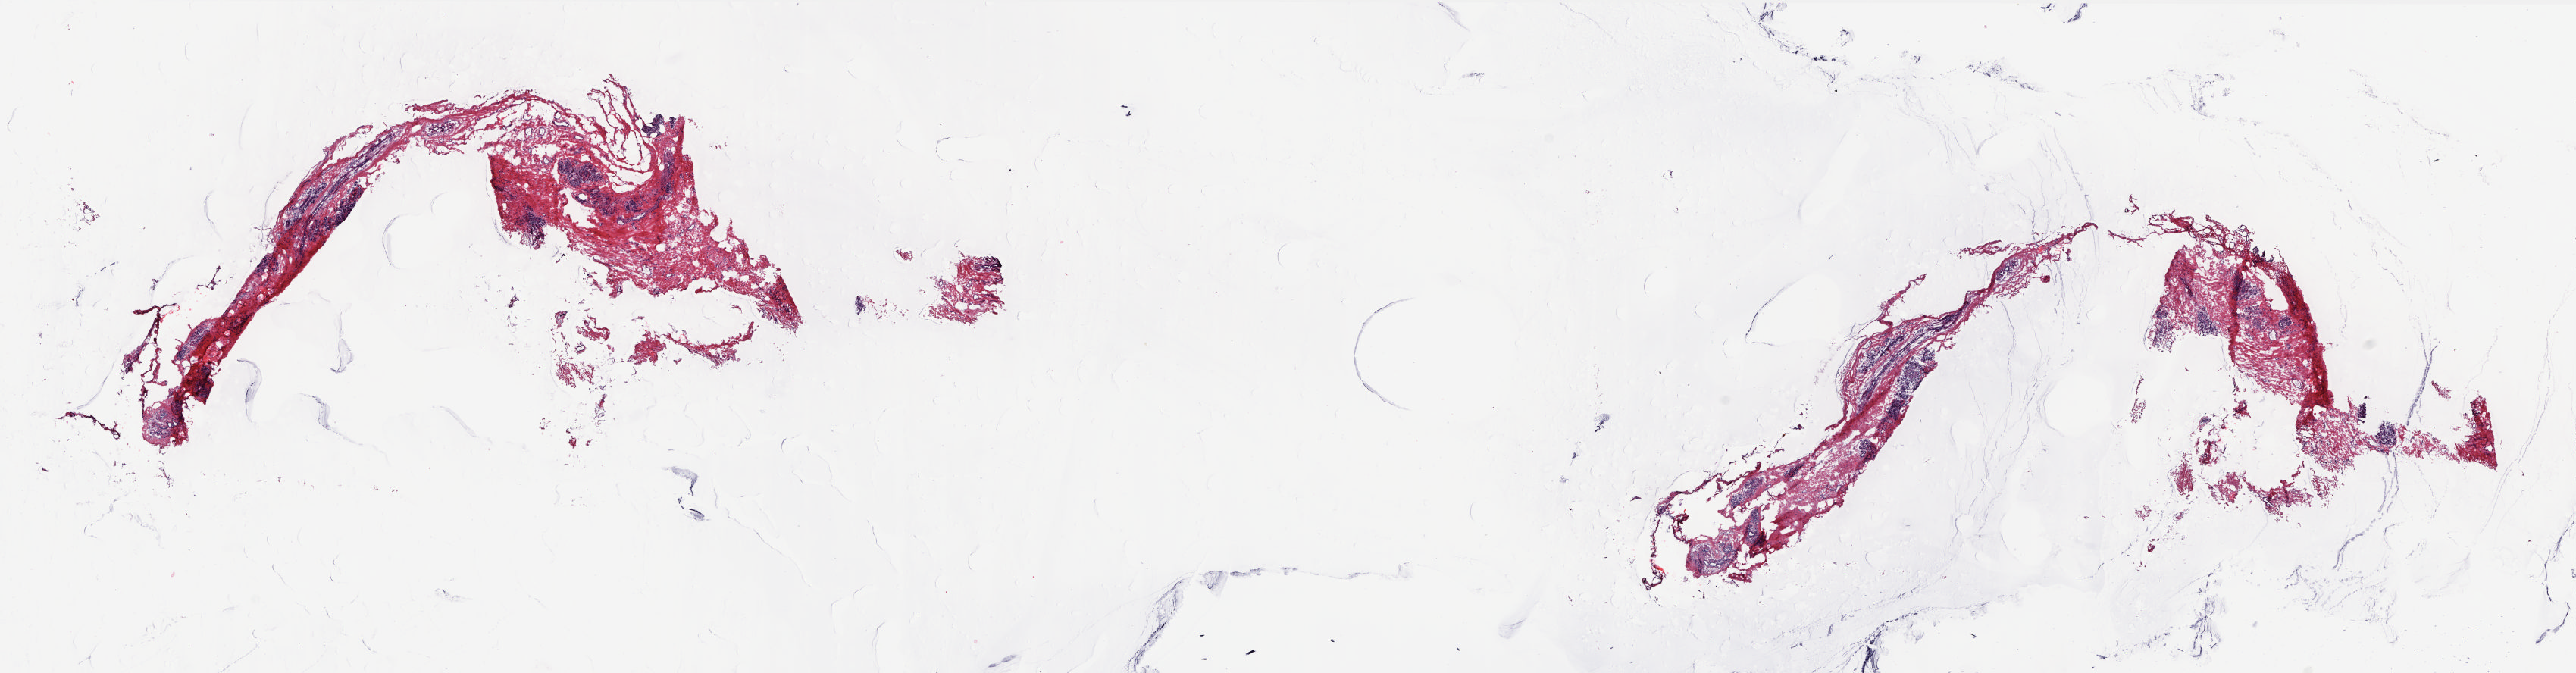
Whole-slide histology image, Hematoxylin and eosin (H&E) stained — shown as a low-resolution overview of the whole scanned area (about 27.4 x 7.2 mm). Frozen section from the top of the tissue portion. Sample: solid tissue normal (non-tumour tissue), breast. Patient: female, age at initial diagnosis 52 years. Pathologist review of this section (percent, as recorded): tumour cells 0%, tumour nuclei 0%, normal cells 25%, stromal cells 75%, necrosis 0%. Infiltration values recorded for this section: lymphocyte infiltration 2%, monocyte infiltration 0%, neutrophil infiltration 0%.
This section: solid tissue normal sample (biorepository sample class). Patient diagnosis: Infiltrating duct carcinoma, NOS.